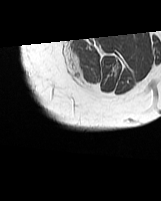
MRI of an extremity soft-tissue mass, one axial slice; MR volume resampled by the dataset authors to the PET/CT grid (not the native acquisition matrix); 161 × 201 image matrix, field of view 157 × 196 mm. Female patient. From the clinical record (not read from this slice): histological type: synovial sarcoma; grade: intermediate; site of the primary tumour: right buttock.
Structures marked on this image (expert contour drawn on MRI and transferred to this co-registered scan by the dataset authors):
- gross tumour volume including surrounding oedema: bounding box <63,45,82,80> (left, top, right, bottom; pixels)